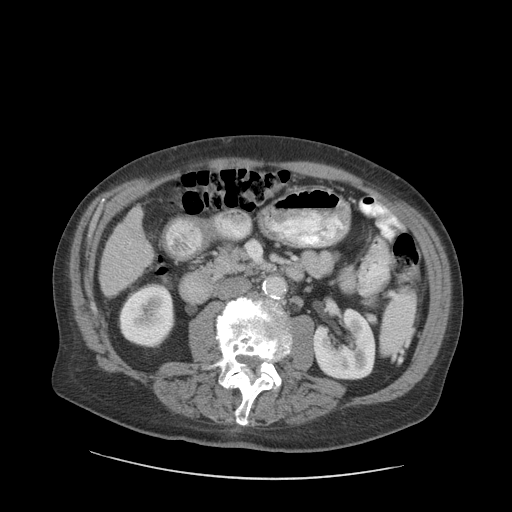
Contrast-enhanced abdominal CT (liver protocol), one axial slice. Soft-tissue window (W 400 / L 40 HU). 2.5 mm slice thickness. 512 × 512 image matrix. Case-level facts recorded for this patient, not image findings: diagnosis: hepatocellular carcinoma (patient treated with transarterial chemoembolisation; whether this scan precedes or follows treatment is not stated here); TNM stage (as recorded): Stage-I; Child-Pugh class: A; tumour differentiation: moderately differentiated; tumour nodularity: uninodular.
Annotated regions visible in this slice (semi-automatically segmented with operator editing):
- liver parenchyma outside the tumour (the mass and vessels are separate outlines, so this box may not span the whole liver): box from (x=100, y=207) to (x=152, y=296) px
- liver vessels: (x=129, y=242)–(x=131, y=245)